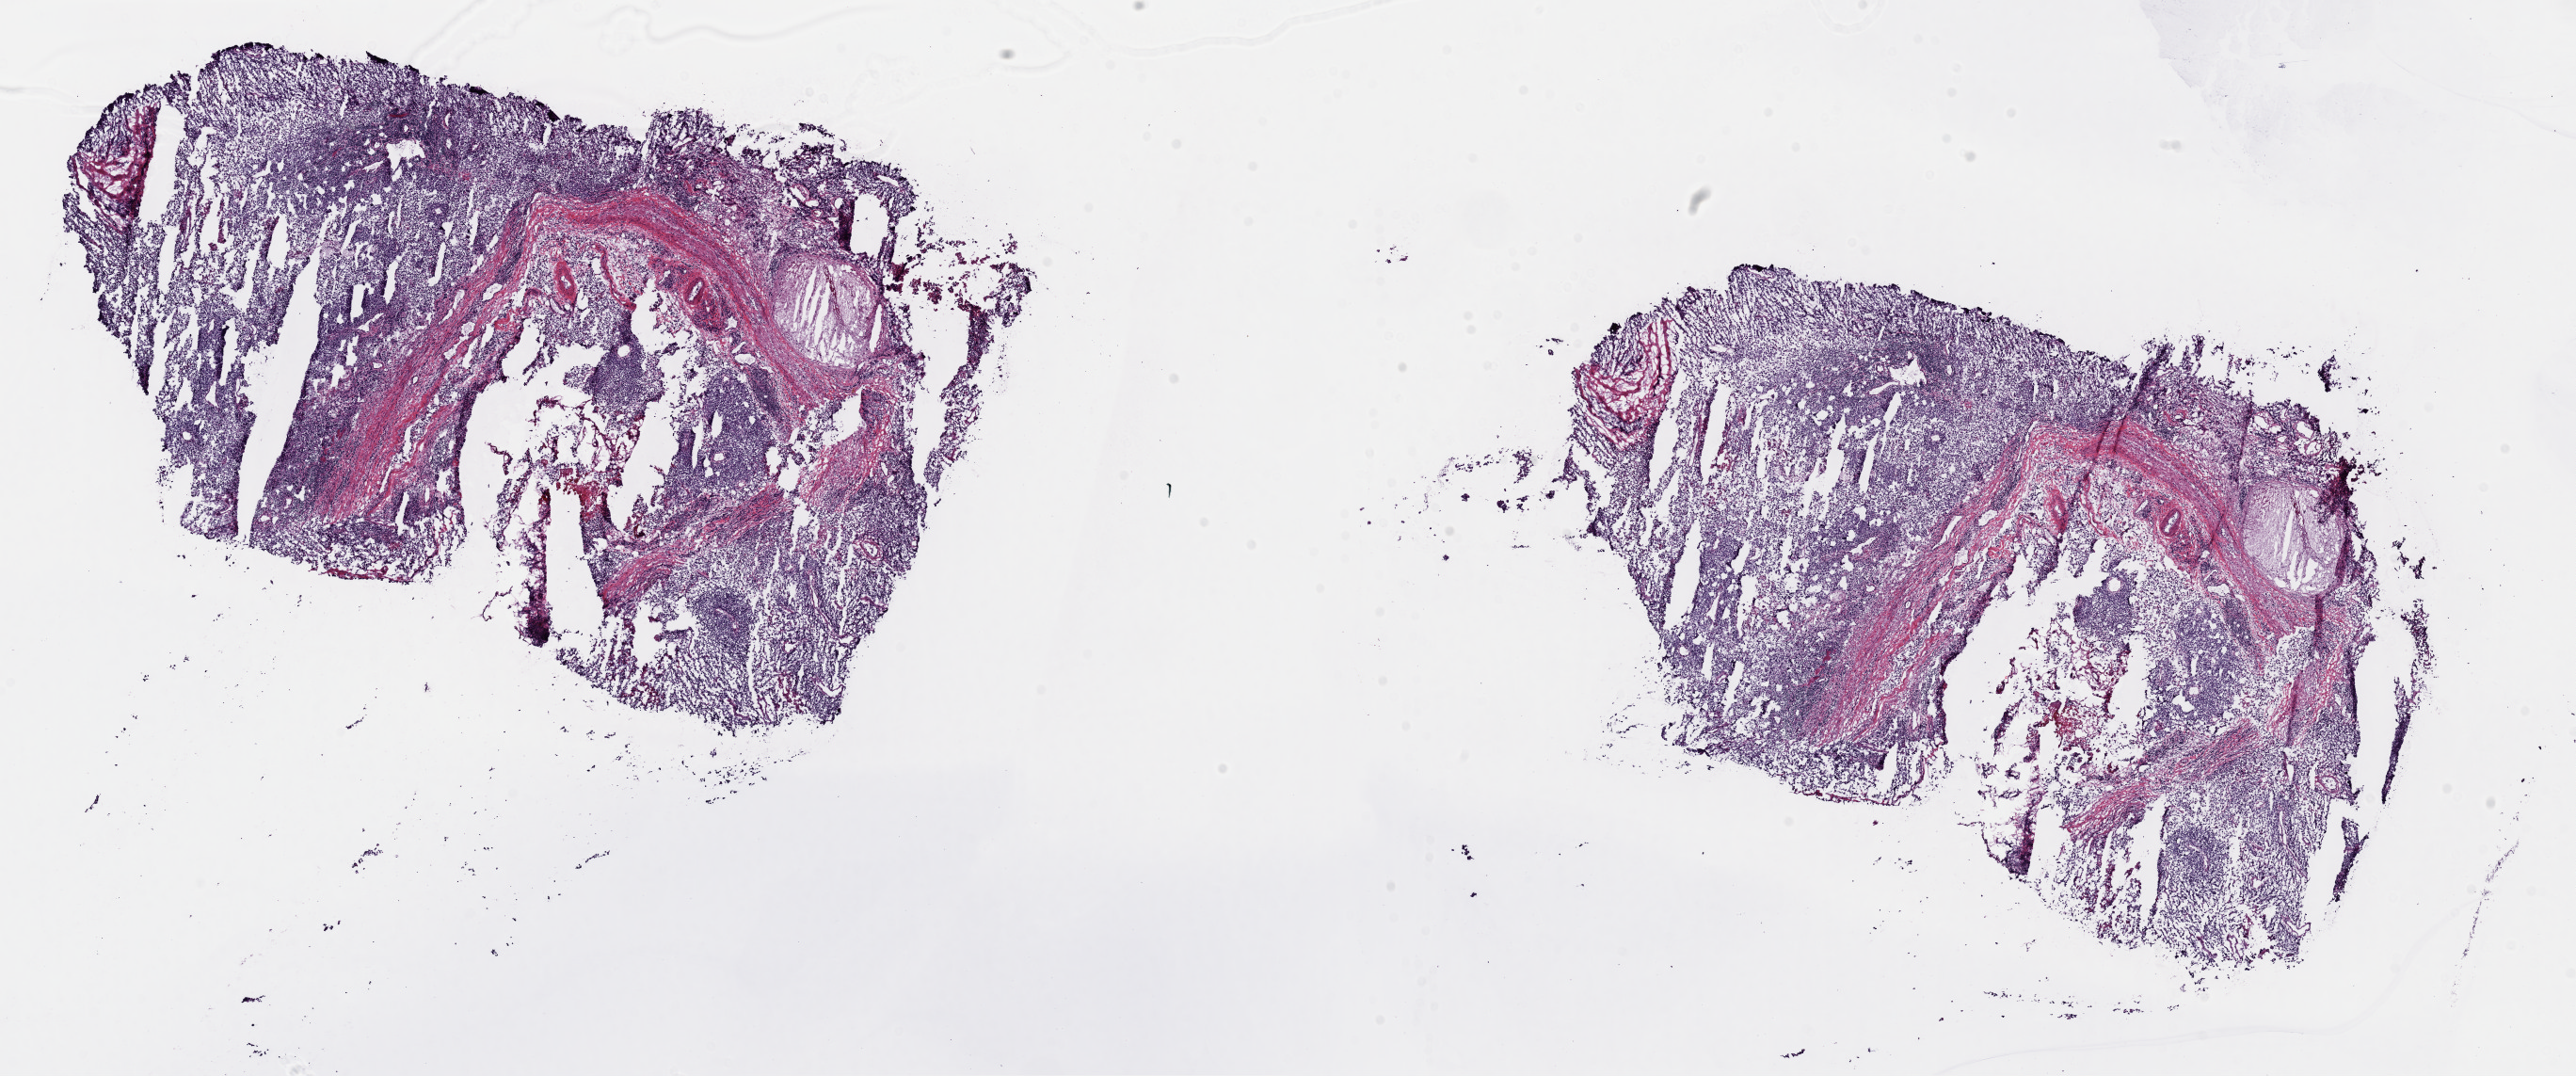
Digitized H&E tissue section (whole slide) — whole scanned area (about 21.6 x 9.0 mm) shown as a low-resolution overview; frozen section from the top of the tissue portion; metastatic tumour sample, sampled site: lymph node. Male, age 55 years at initial diagnosis. Composition of this section per pathologist review: tumour cells 90%, tumour nuclei 85%.
This section: metastatic tumour tissue. Patient diagnosis: Malignant melanoma, NOS.